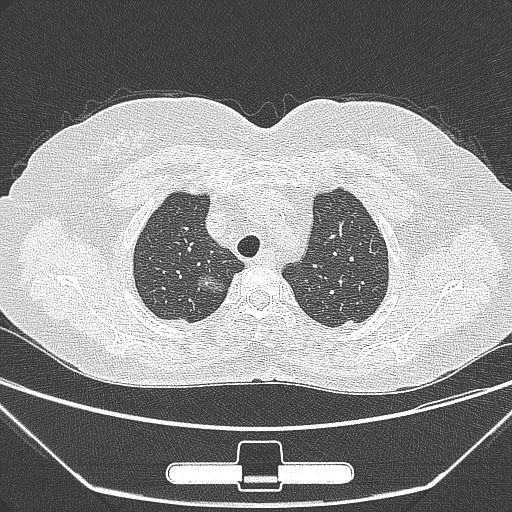
Chest CT, one axial slice; slice 230 of 275 in the series (ordered by position); lung window (W 1500 / L -600 HU); 1 mm slice thickness; 512 × 512 image matrix, field of view 356 × 356 mm. Female patient, age 63 years. Case-level facts recorded for this patient, not image findings: clinical TNM (as recorded): T1a N0 M0; histopathological grade: G1.
Outlined on this slice (rectangle marked by the reading radiologist):
- lung tumour (recorded histology: adenocarcinoma): bounding box [x1, y1, x2, y2] px = [192, 268, 234, 300]